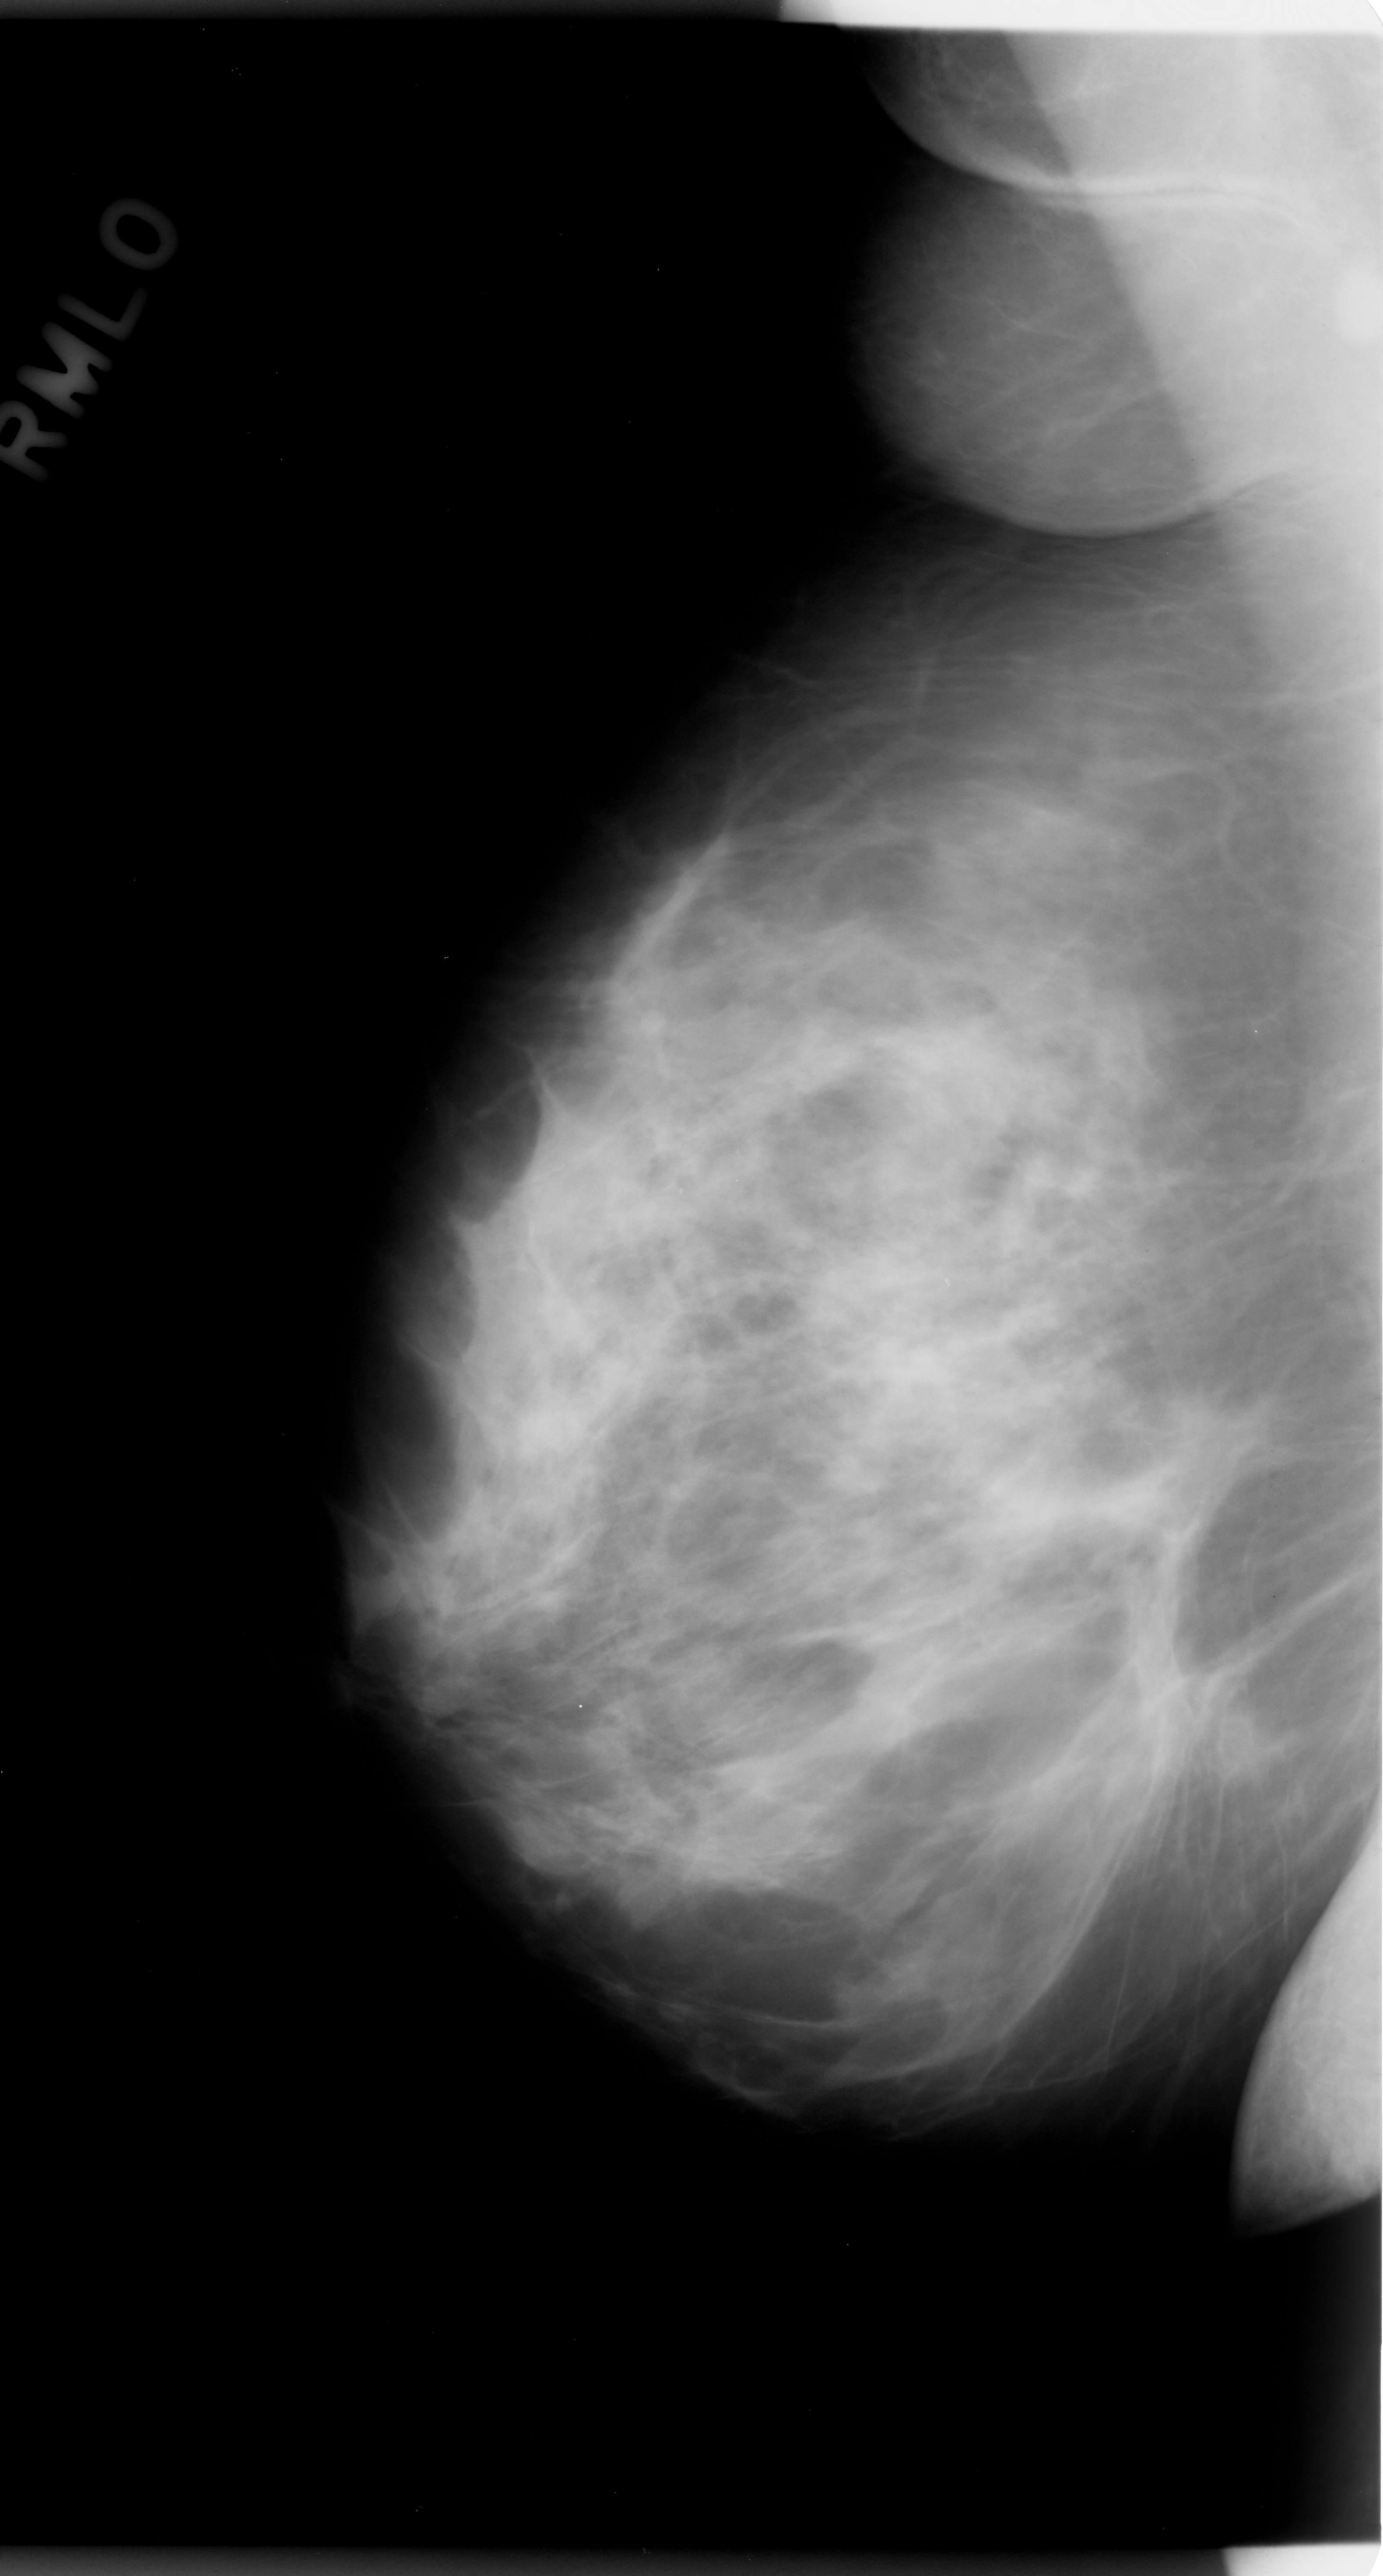
Digitized screen-film mammogram; right breast; mediolateral oblique (MLO) view.
- Abnormality record for this image: mass, shape architectural distortion, margins ill defined; BI-RADS assessment category 5; subtlety rating 5 on a 1 (subtle) to 5 (obvious) scale; pathology (as recorded): malignant.